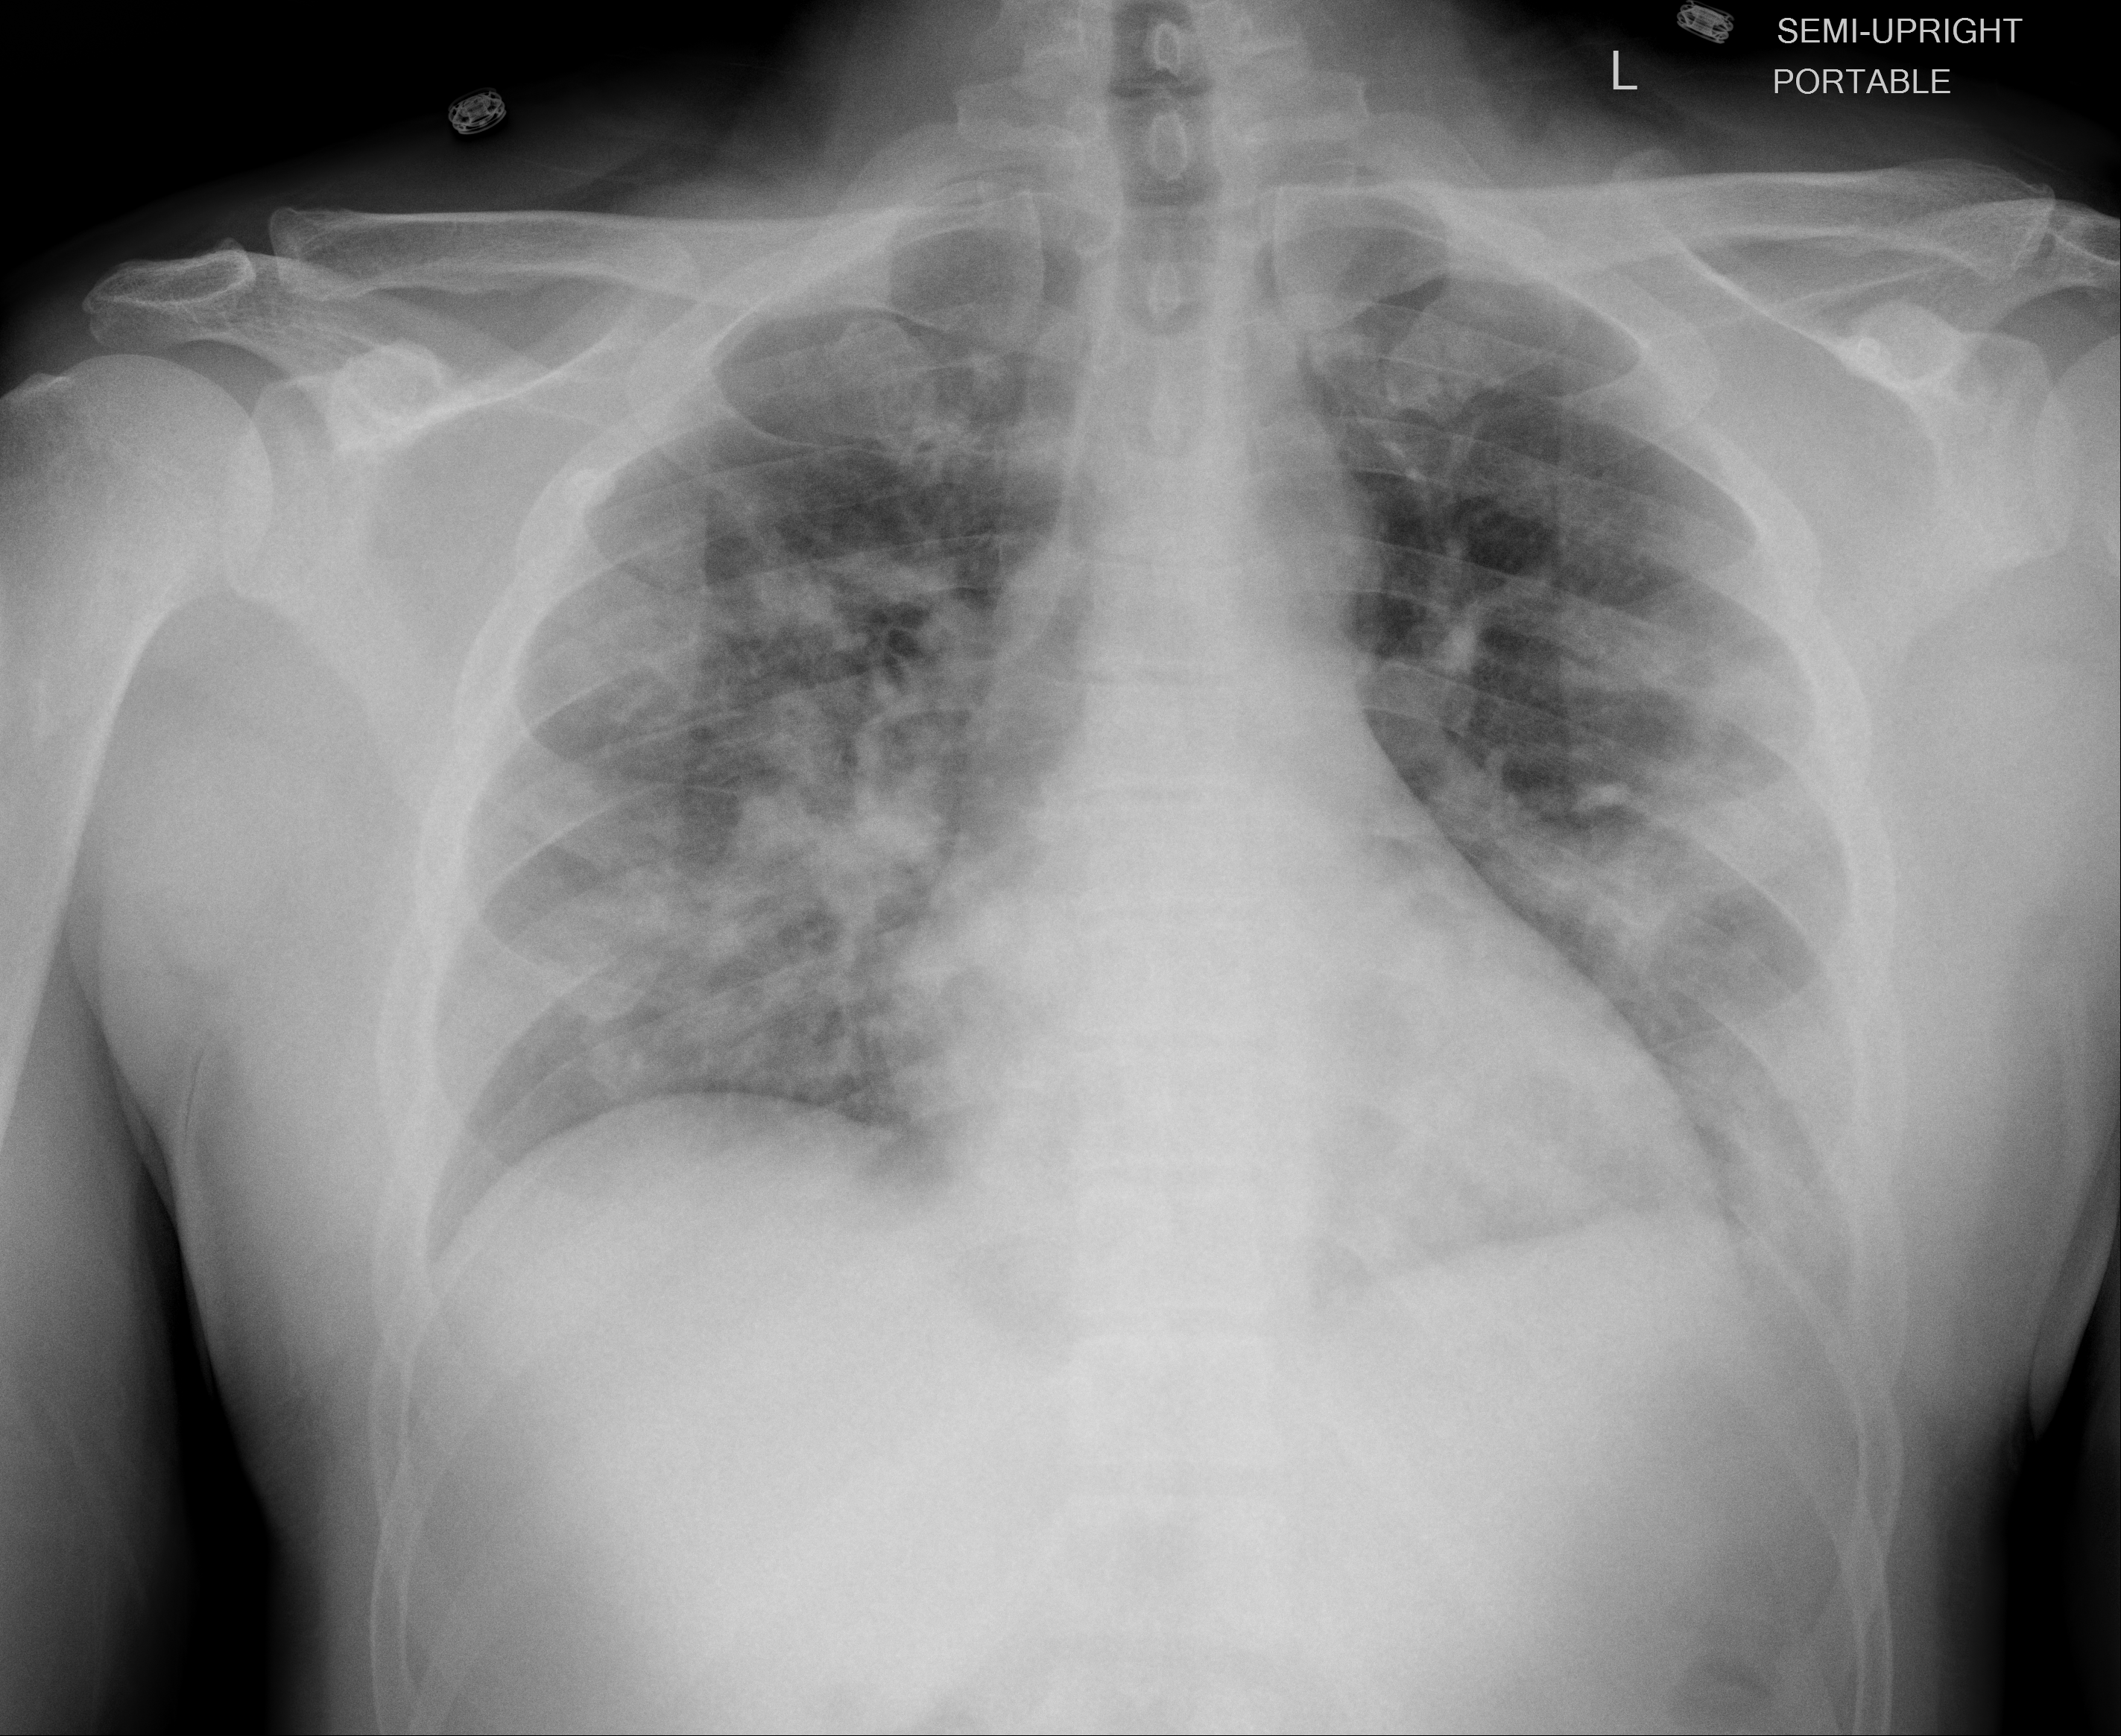
Chest X-ray, AP projection. Male patient, age 48 years; COVID-19 (test-positive).
Radiologist key findings (as recorded): patchy opacities throughout both lungs, not significantly changed from the prior examination.